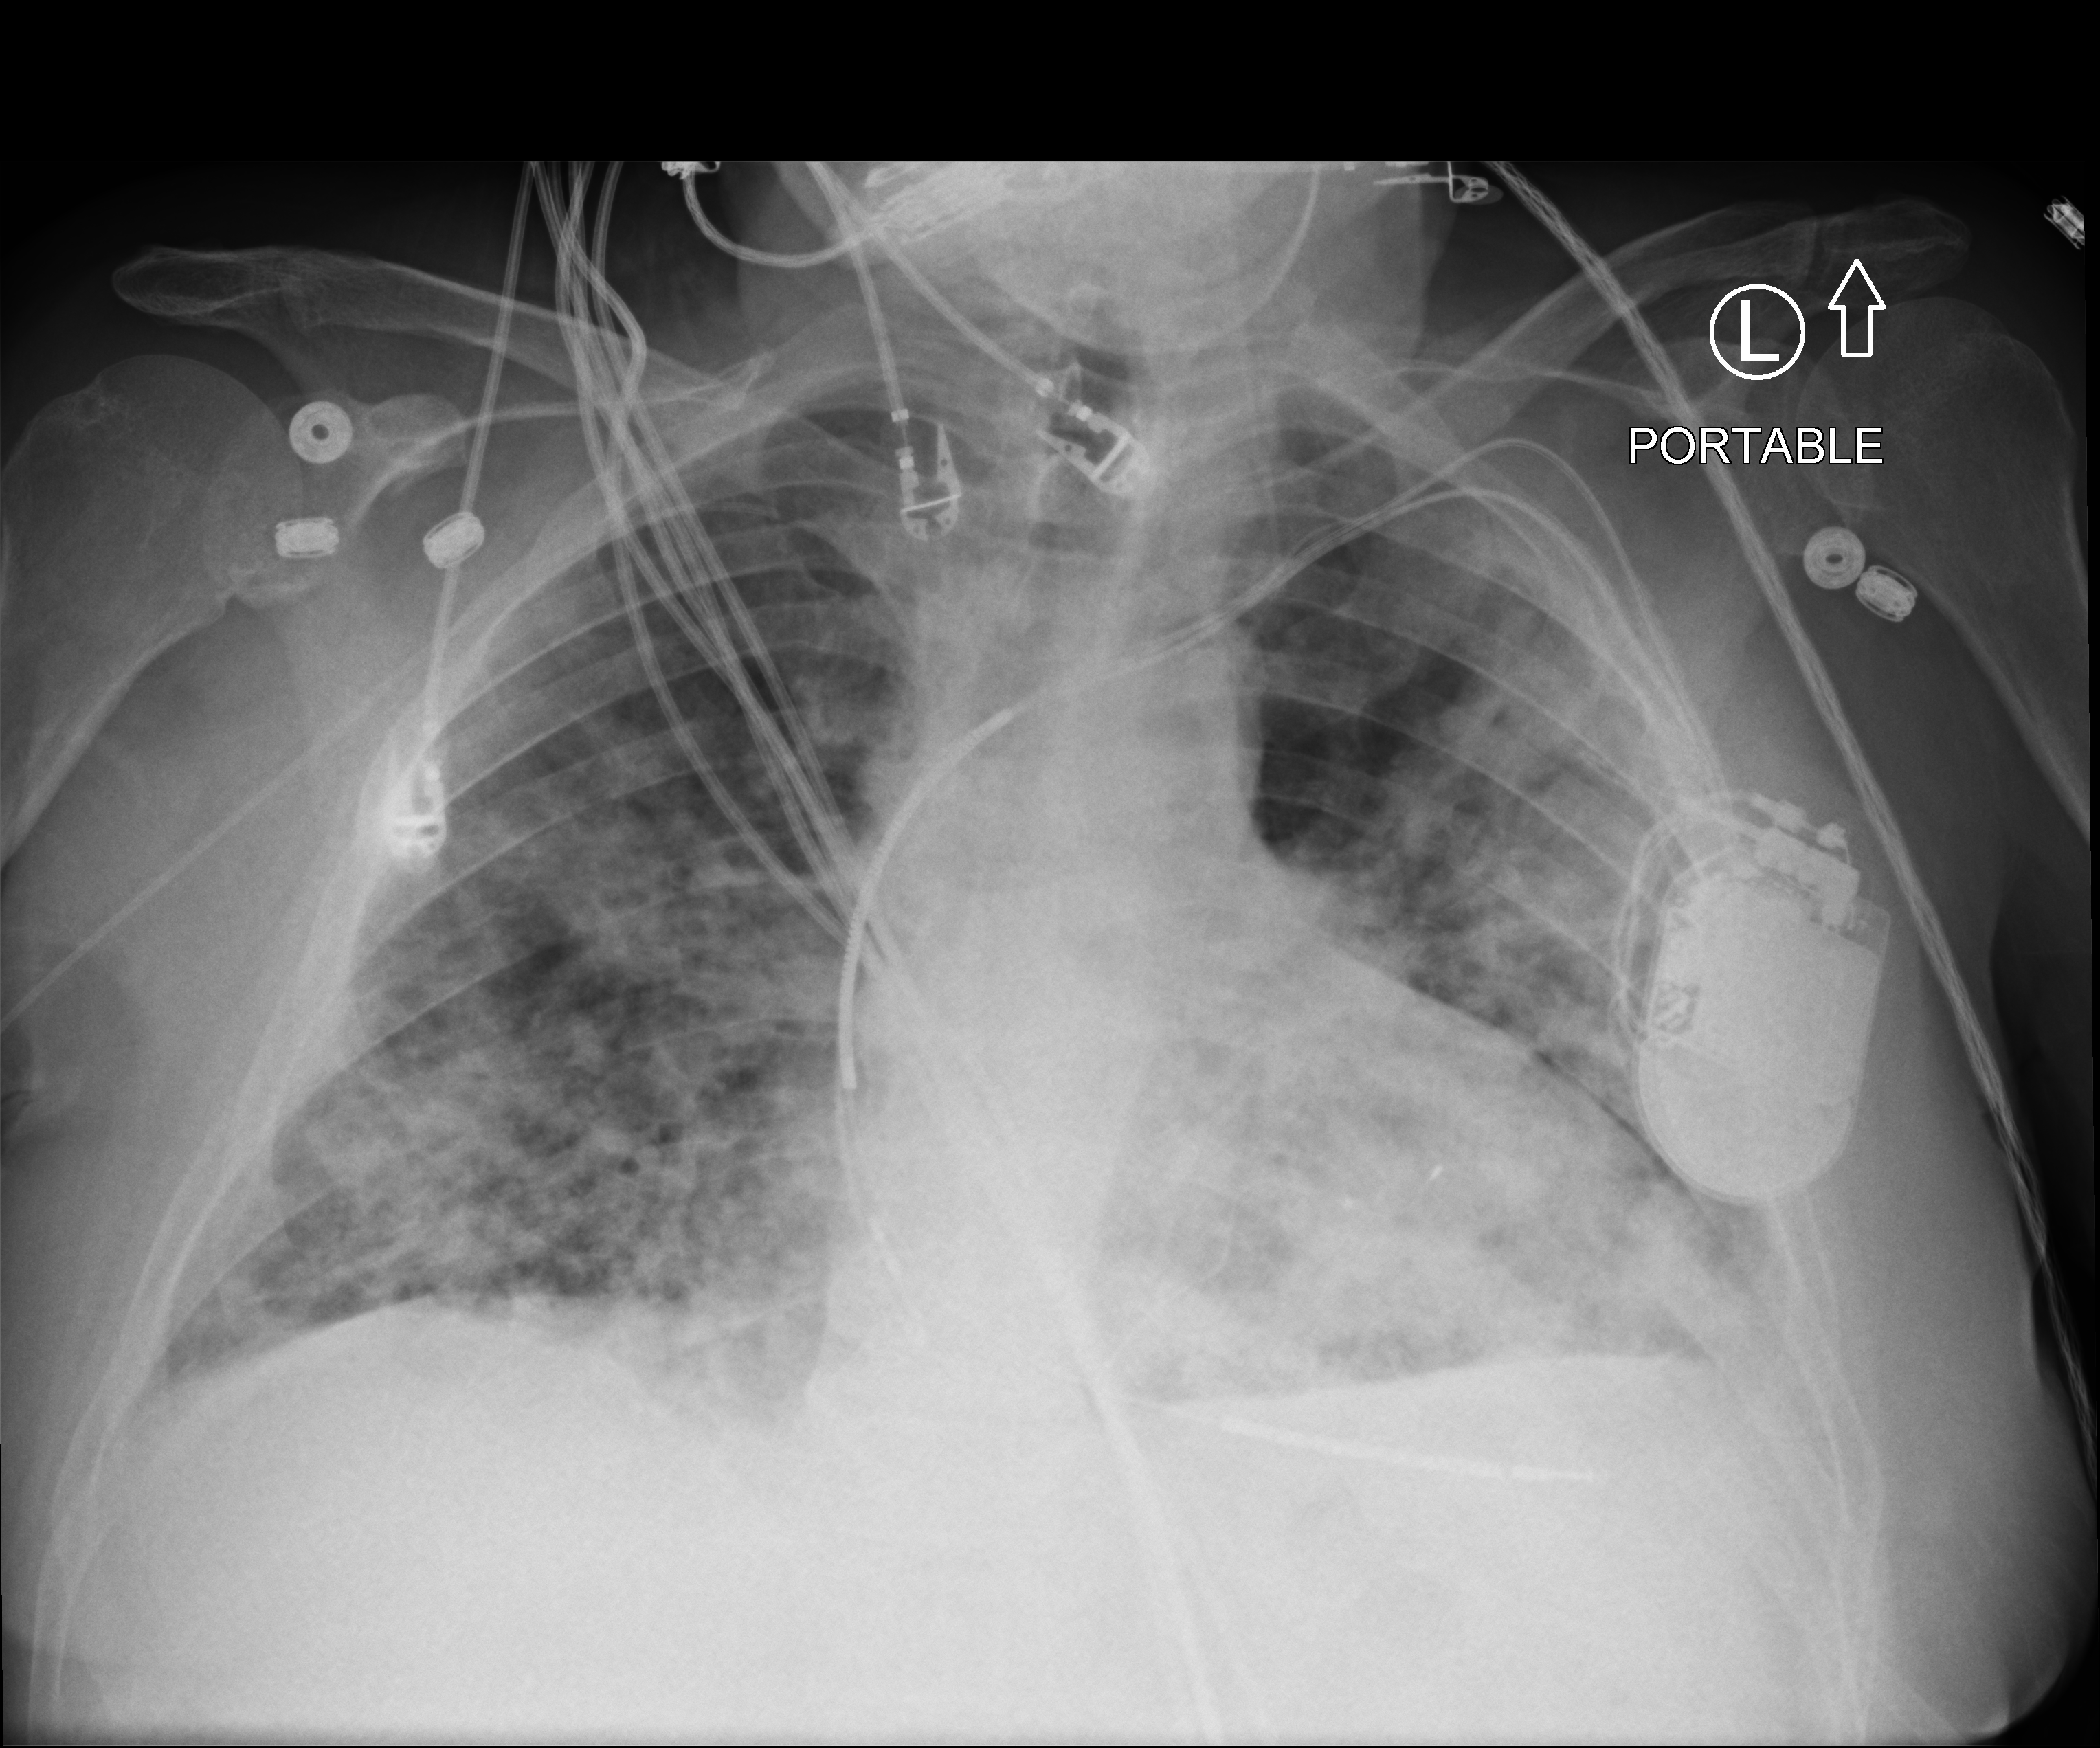
Bedside chest radiograph (computed radiography), anteroposterior (AP) projection. Patient hospitalised with COVID-19; male, aged 60–74 years.
Admission-level facts for this patient (not findings on this image; timing relative to this image not recorded): mechanically ventilated during this hospital stay: no.